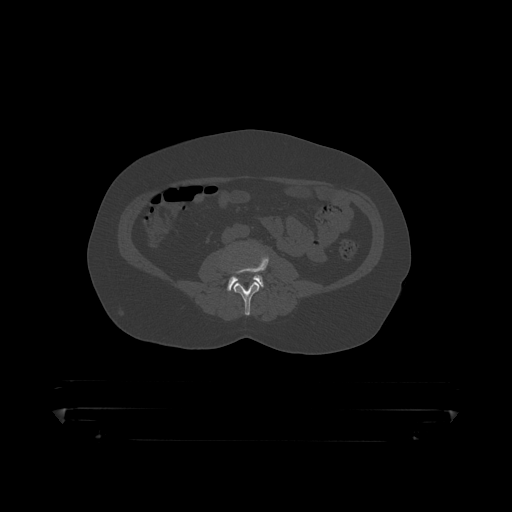
CT including the spine, one axial slice; slice 80 of 390 in the series (ordered by position); 120 kVp; bone window (W 1800 / L 400 HU); 1.25 mm slice thickness; 512 × 512 image matrix, field of view 650 × 650 mm. Patient: male, 60 years. From the clinical record (not read from this slice): primary cancer: prostate.
Structures marked on this image (semi-automatic segmentation, software-assisted and operator-edited):
- L3 vertebra: bounding box [x1, y1, x2, y2] px = [225, 251, 269, 316]
- L4 vertebra: [227, 275, 264, 292]